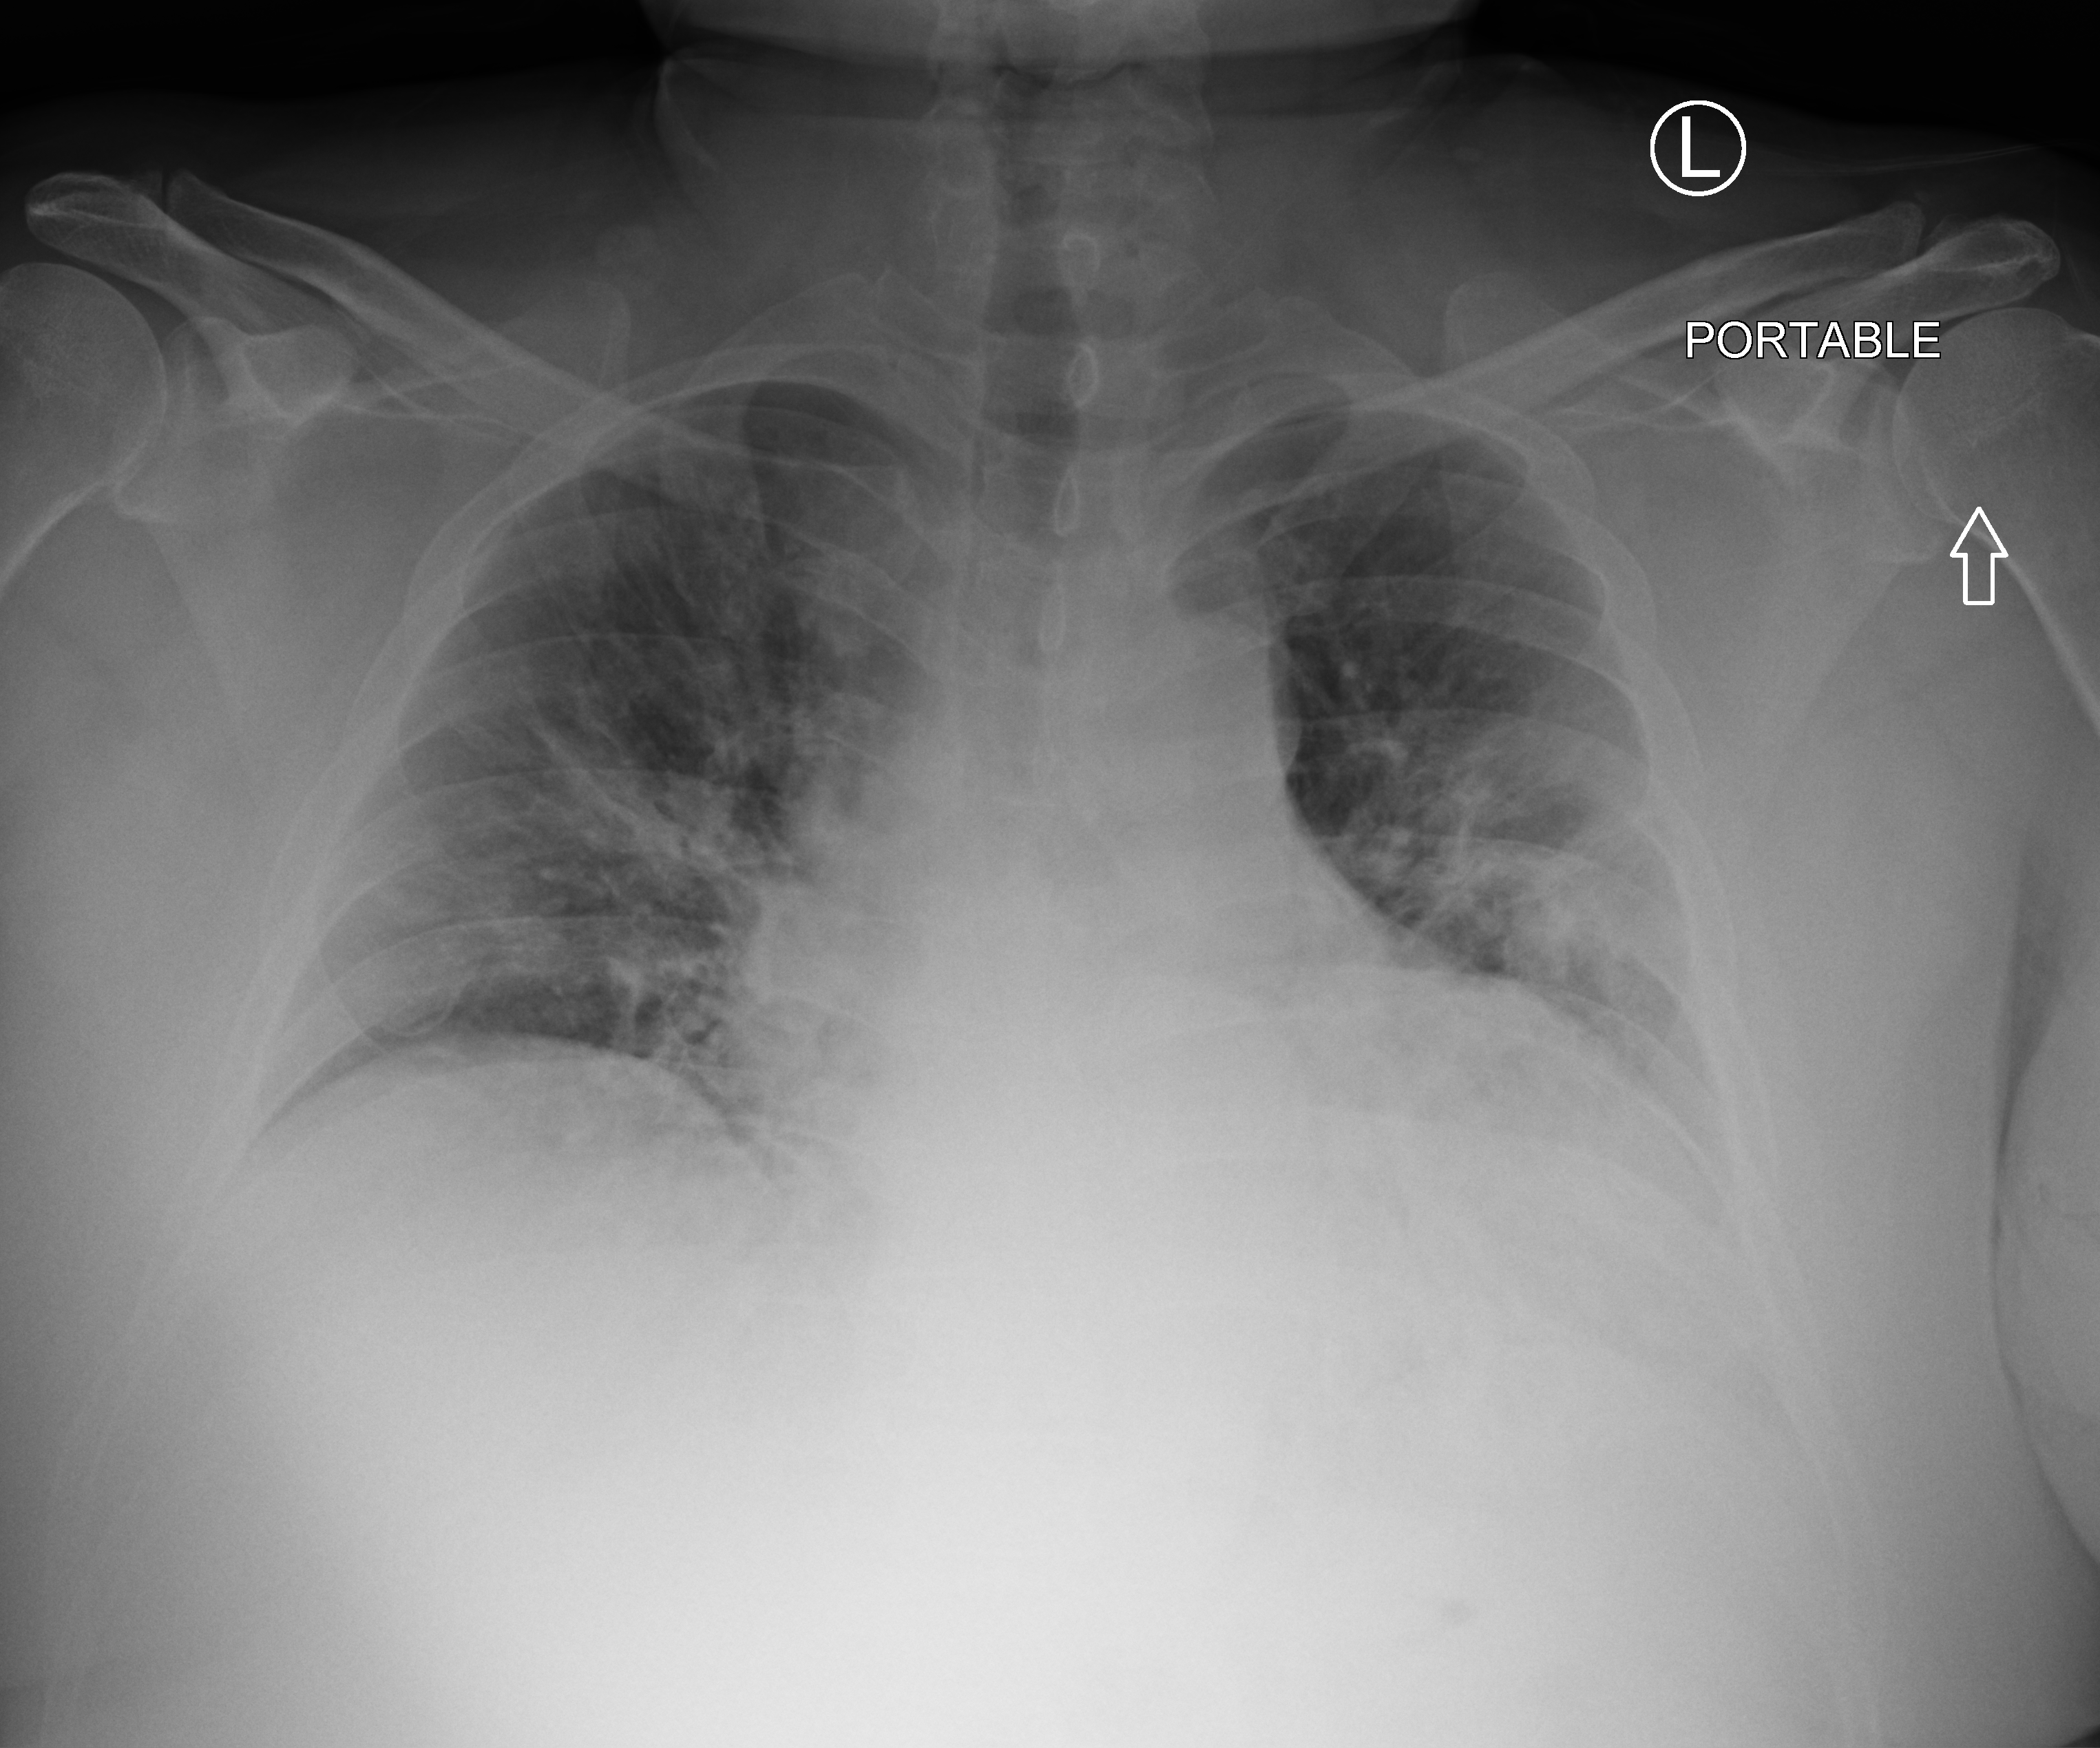
Chest X-ray (portable), anteroposterior (AP) projection. Patient hospitalised with COVID-19; male, aged 18–59 years.
Admission-level facts for this patient (not findings on this image; timing relative to this image not recorded): chronic kidney disease (admission record): no.